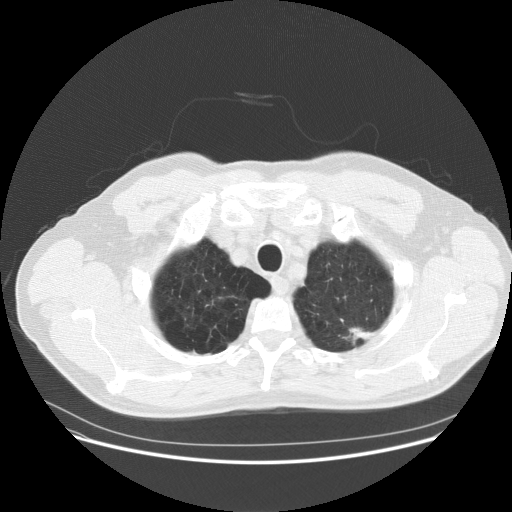
Axial slice from a low-dose chest CT screening exam; first (baseline) screen; lung window (W 1500 / L -600 HU); standard (soft-tissue) reconstruction kernel (STANDARD); slice 14 of 158 in the series; 512 × 512 image matrix, field of view 400 × 400 mm. Male participant, aged 61 years at enrolment. Current smoker at enrolment.
- Lesion marked by an expert reader, bounding box [x1, y1, x2, y2] px = [326, 309, 391, 363].
- Reader record for this screening exam (exam-level; its link to the box is not recorded): non-calcified nodule or mass ≥4 mm, left upper lobe, 12 × 6 mm, poorly defined margins, soft tissue attenuation.
- Later outcome: lung cancer diagnosed 317 days after this screen — adenocarcinoma, NOS, left upper lobe, poorly differentiated (G3), stage IIIA (AJCC 6th edition), 30 mm at pathology.